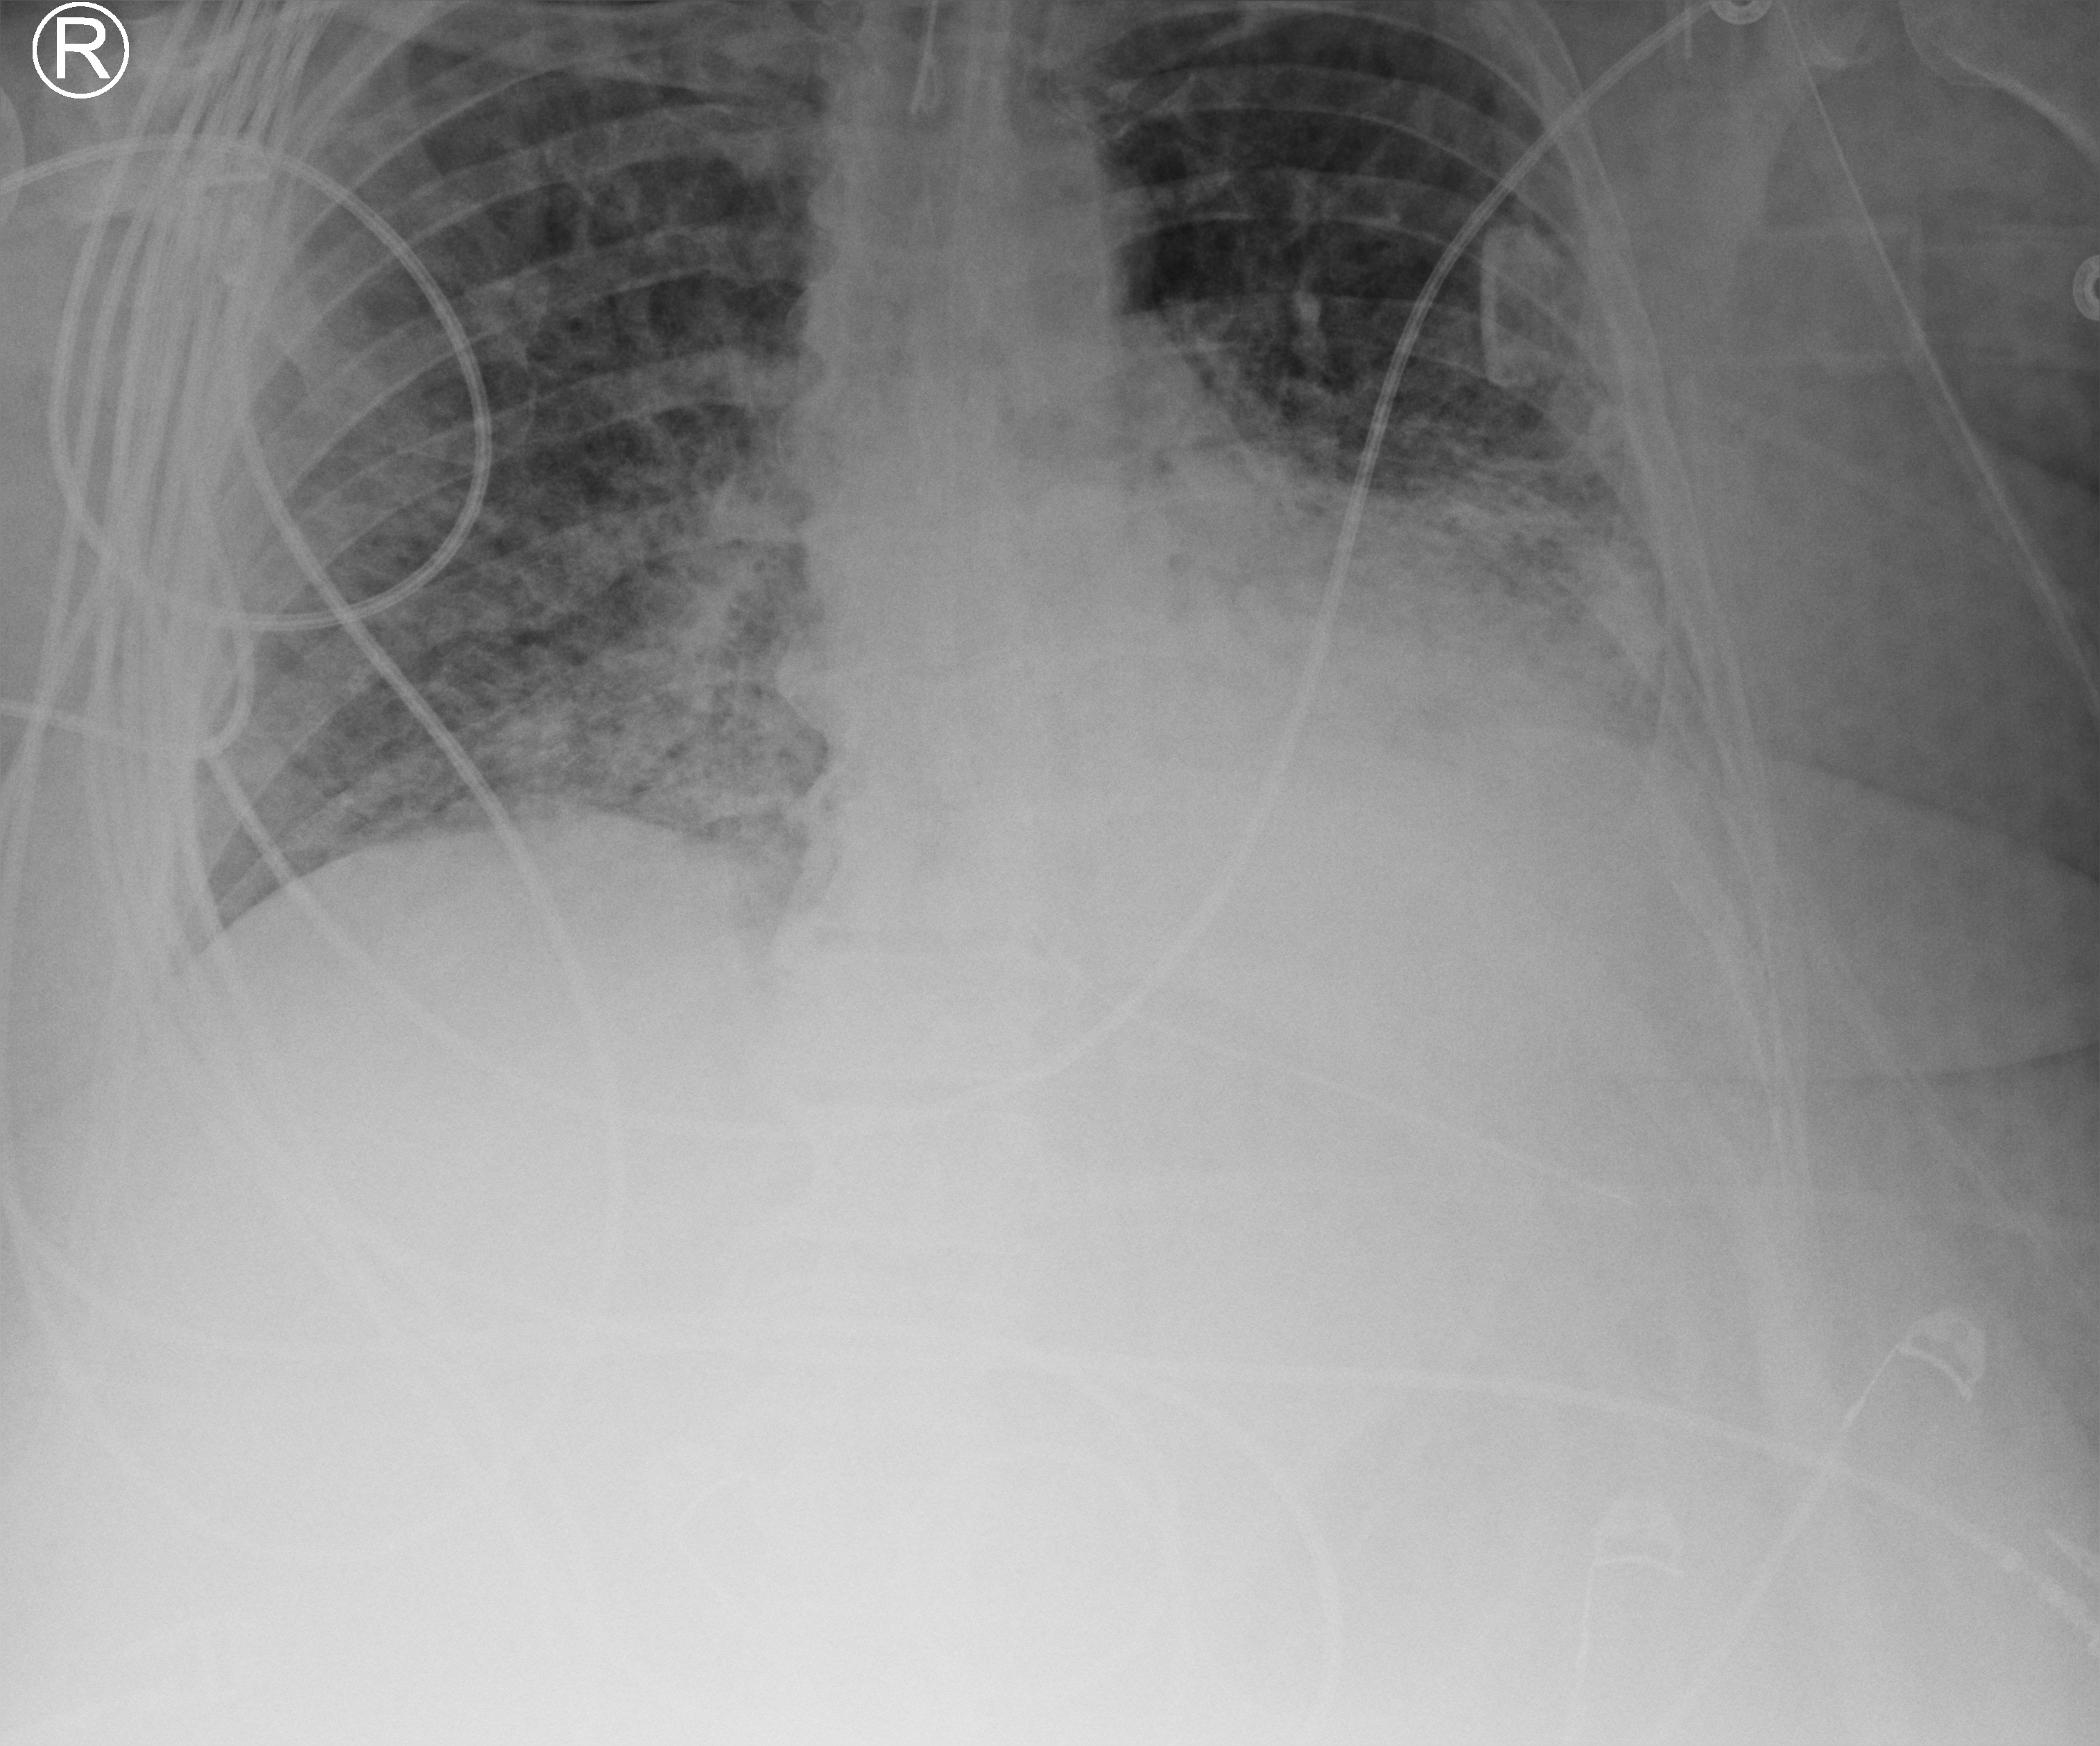
Bedside chest radiograph (computed radiography); anteroposterior (AP) projection. Patient hospitalised with COVID-19, aged 18–59 years.
Hospital-stay facts (about this admission, not read from this image; timing relative to this image not recorded): mechanically ventilated during this hospital stay: yes; admitted to intensive care during this hospital stay: yes.